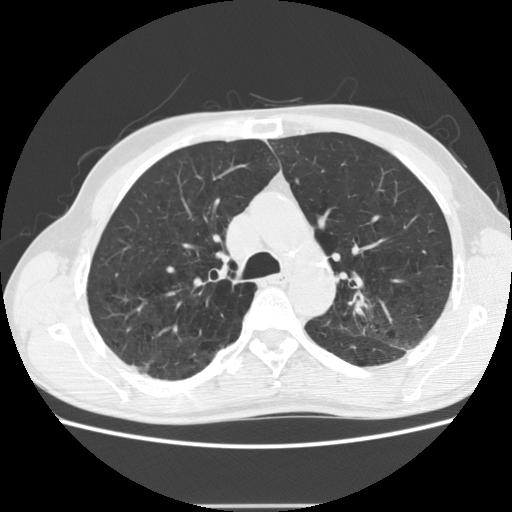
Low-dose screening chest CT, one axial slice; reconstruction kernel STANDARD; lung window (W 1500 / L -600 HU); 2.5 mm slice thickness; 512 × 512 image matrix, field of view 352 × 352 mm.
Structures marked on this image (manually delineated by an expert):
- lesion 1 (tumor, upper lobe of left lung): bounding box <357,302,365,314> (left, top, right, bottom; pixels)